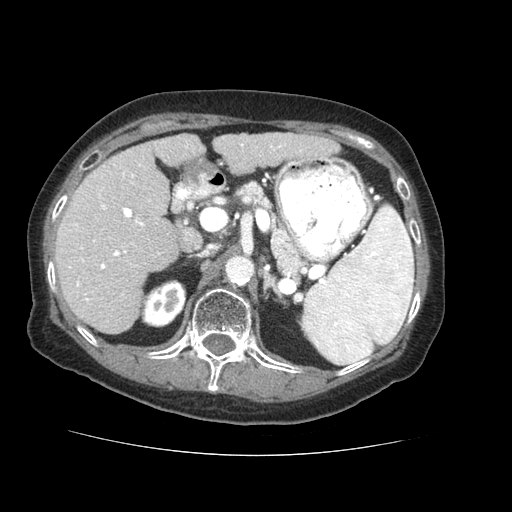
Contrast-enhanced abdominal CT (liver protocol), one axial slice; slice 30 of 73 in the series (ordered by position); reconstruction kernel STANDARD; 120 kVp; soft-tissue window (W 400 / L 40 HU); 2.5 mm slice thickness; 512 × 512 image matrix, field of view 360 × 360 mm. From the clinical record (not read from this slice): diagnosis: hepatocellular carcinoma (patient treated with transarterial chemoembolisation; whether this scan precedes or follows treatment is not stated here); TNM stage (as recorded): Stage-IVB; Child-Pugh class: A; tumour differentiation: well differentiated; tumour nodularity: uninodular.
Annotated regions visible in this slice (semi-automatically segmented with operator editing):
- liver parenchyma outside the tumour (the mass and vessels are separate outlines, so this box may not span the whole liver): box from (x=54, y=132) to (x=338, y=334) px
- liver vessels: (x=69, y=144)–(x=301, y=302)